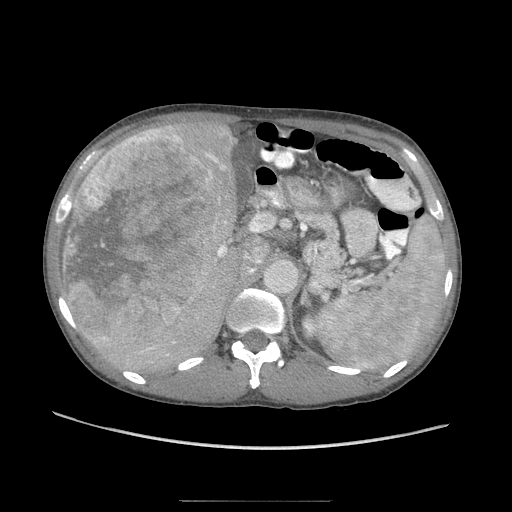
Contrast-enhanced abdominal CT (liver protocol), one axial slice. Slice 53 of 103 in the series (ordered by position). 120 kVp. Soft-tissue window (W 400 / L 40 HU). 512 × 512 image matrix, field of view 380 × 380 mm. From the clinical record (not read from this slice): diagnosis: hepatocellular carcinoma (patient treated with transarterial chemoembolisation; whether this scan precedes or follows treatment is not stated here); TNM stage (as recorded): Stage-IIIA; Child-Pugh class: A; tumour differentiation: moderately differentiated; tumour nodularity: multinodular.
Annotated regions visible in this slice (semi-automatically segmented with operator editing):
- liver parenchyma outside the tumour (the mass and vessels are separate outlines, so this box may not span the whole liver): bounding box <76,120,240,376> (left, top, right, bottom; pixels)
- mass: <61,121,237,344>
- liver vessels: <217,158,223,166>